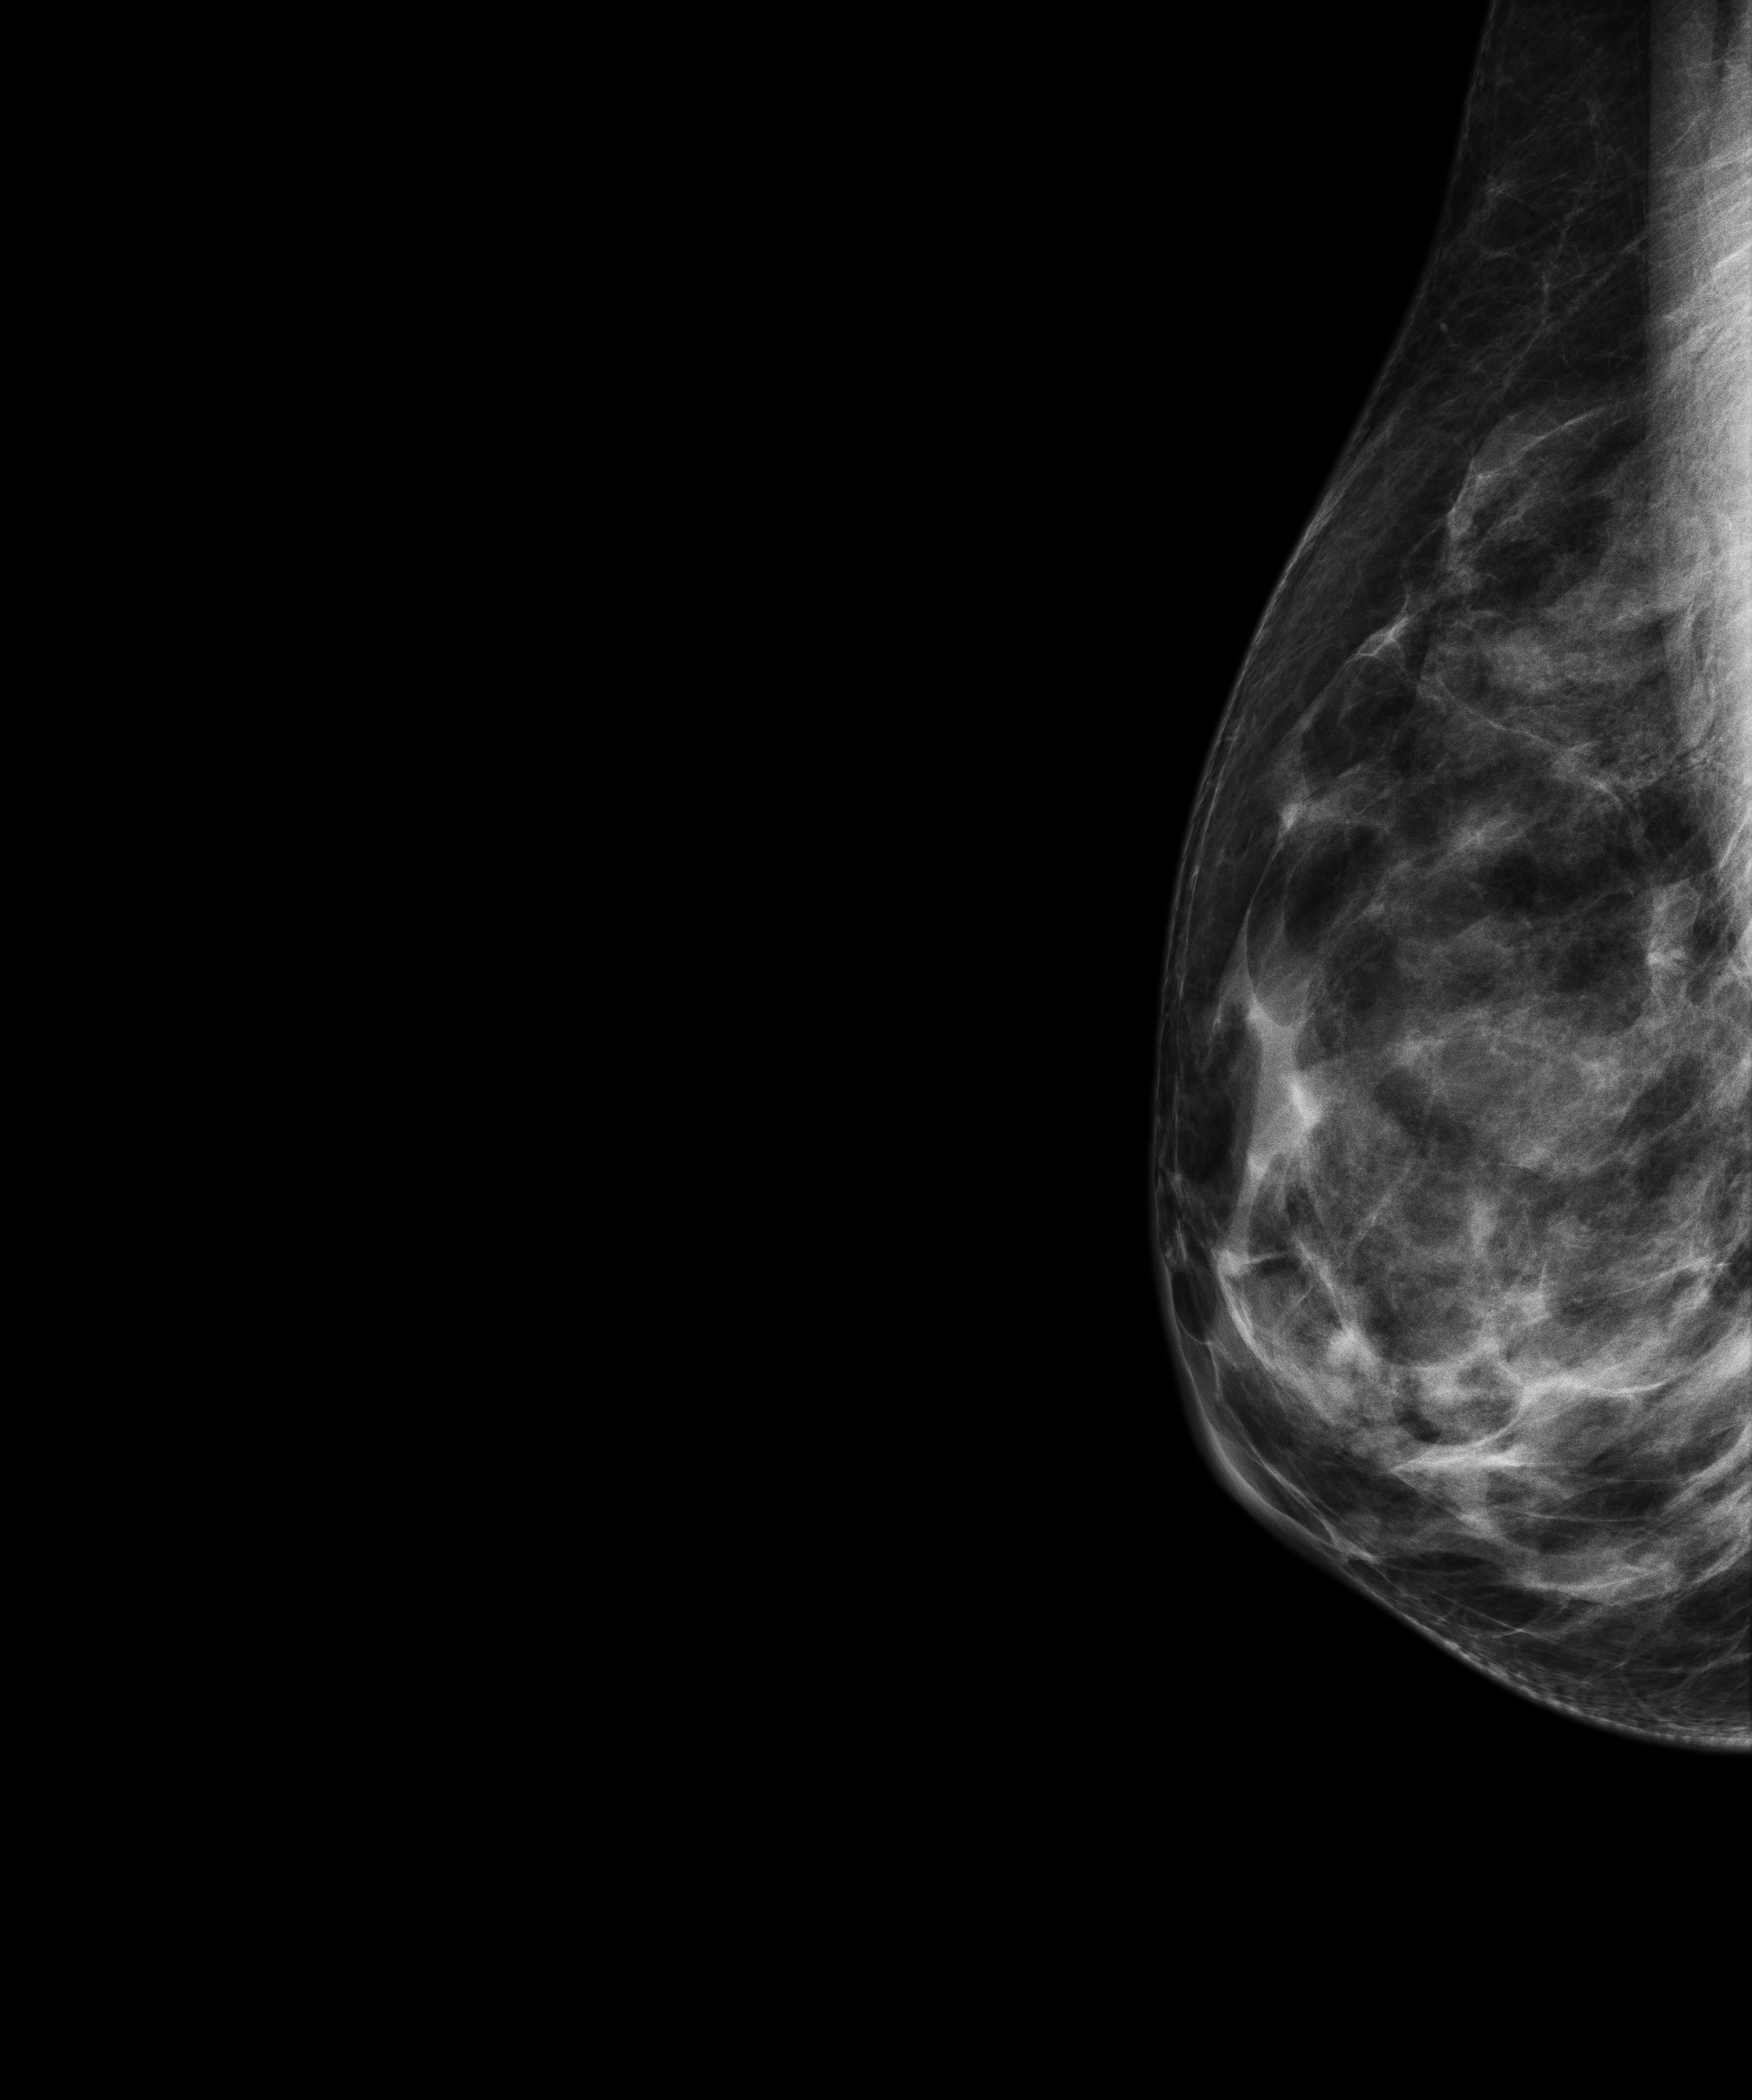
Digital mammogram (FFDM); right breast; laterally exaggerated craniocaudal (XCCL) view; screening examination. Patient aged 66 years (female).
Final BI-RADS assessment for this screening round (tomosynthesis exam, both breasts): category 1.